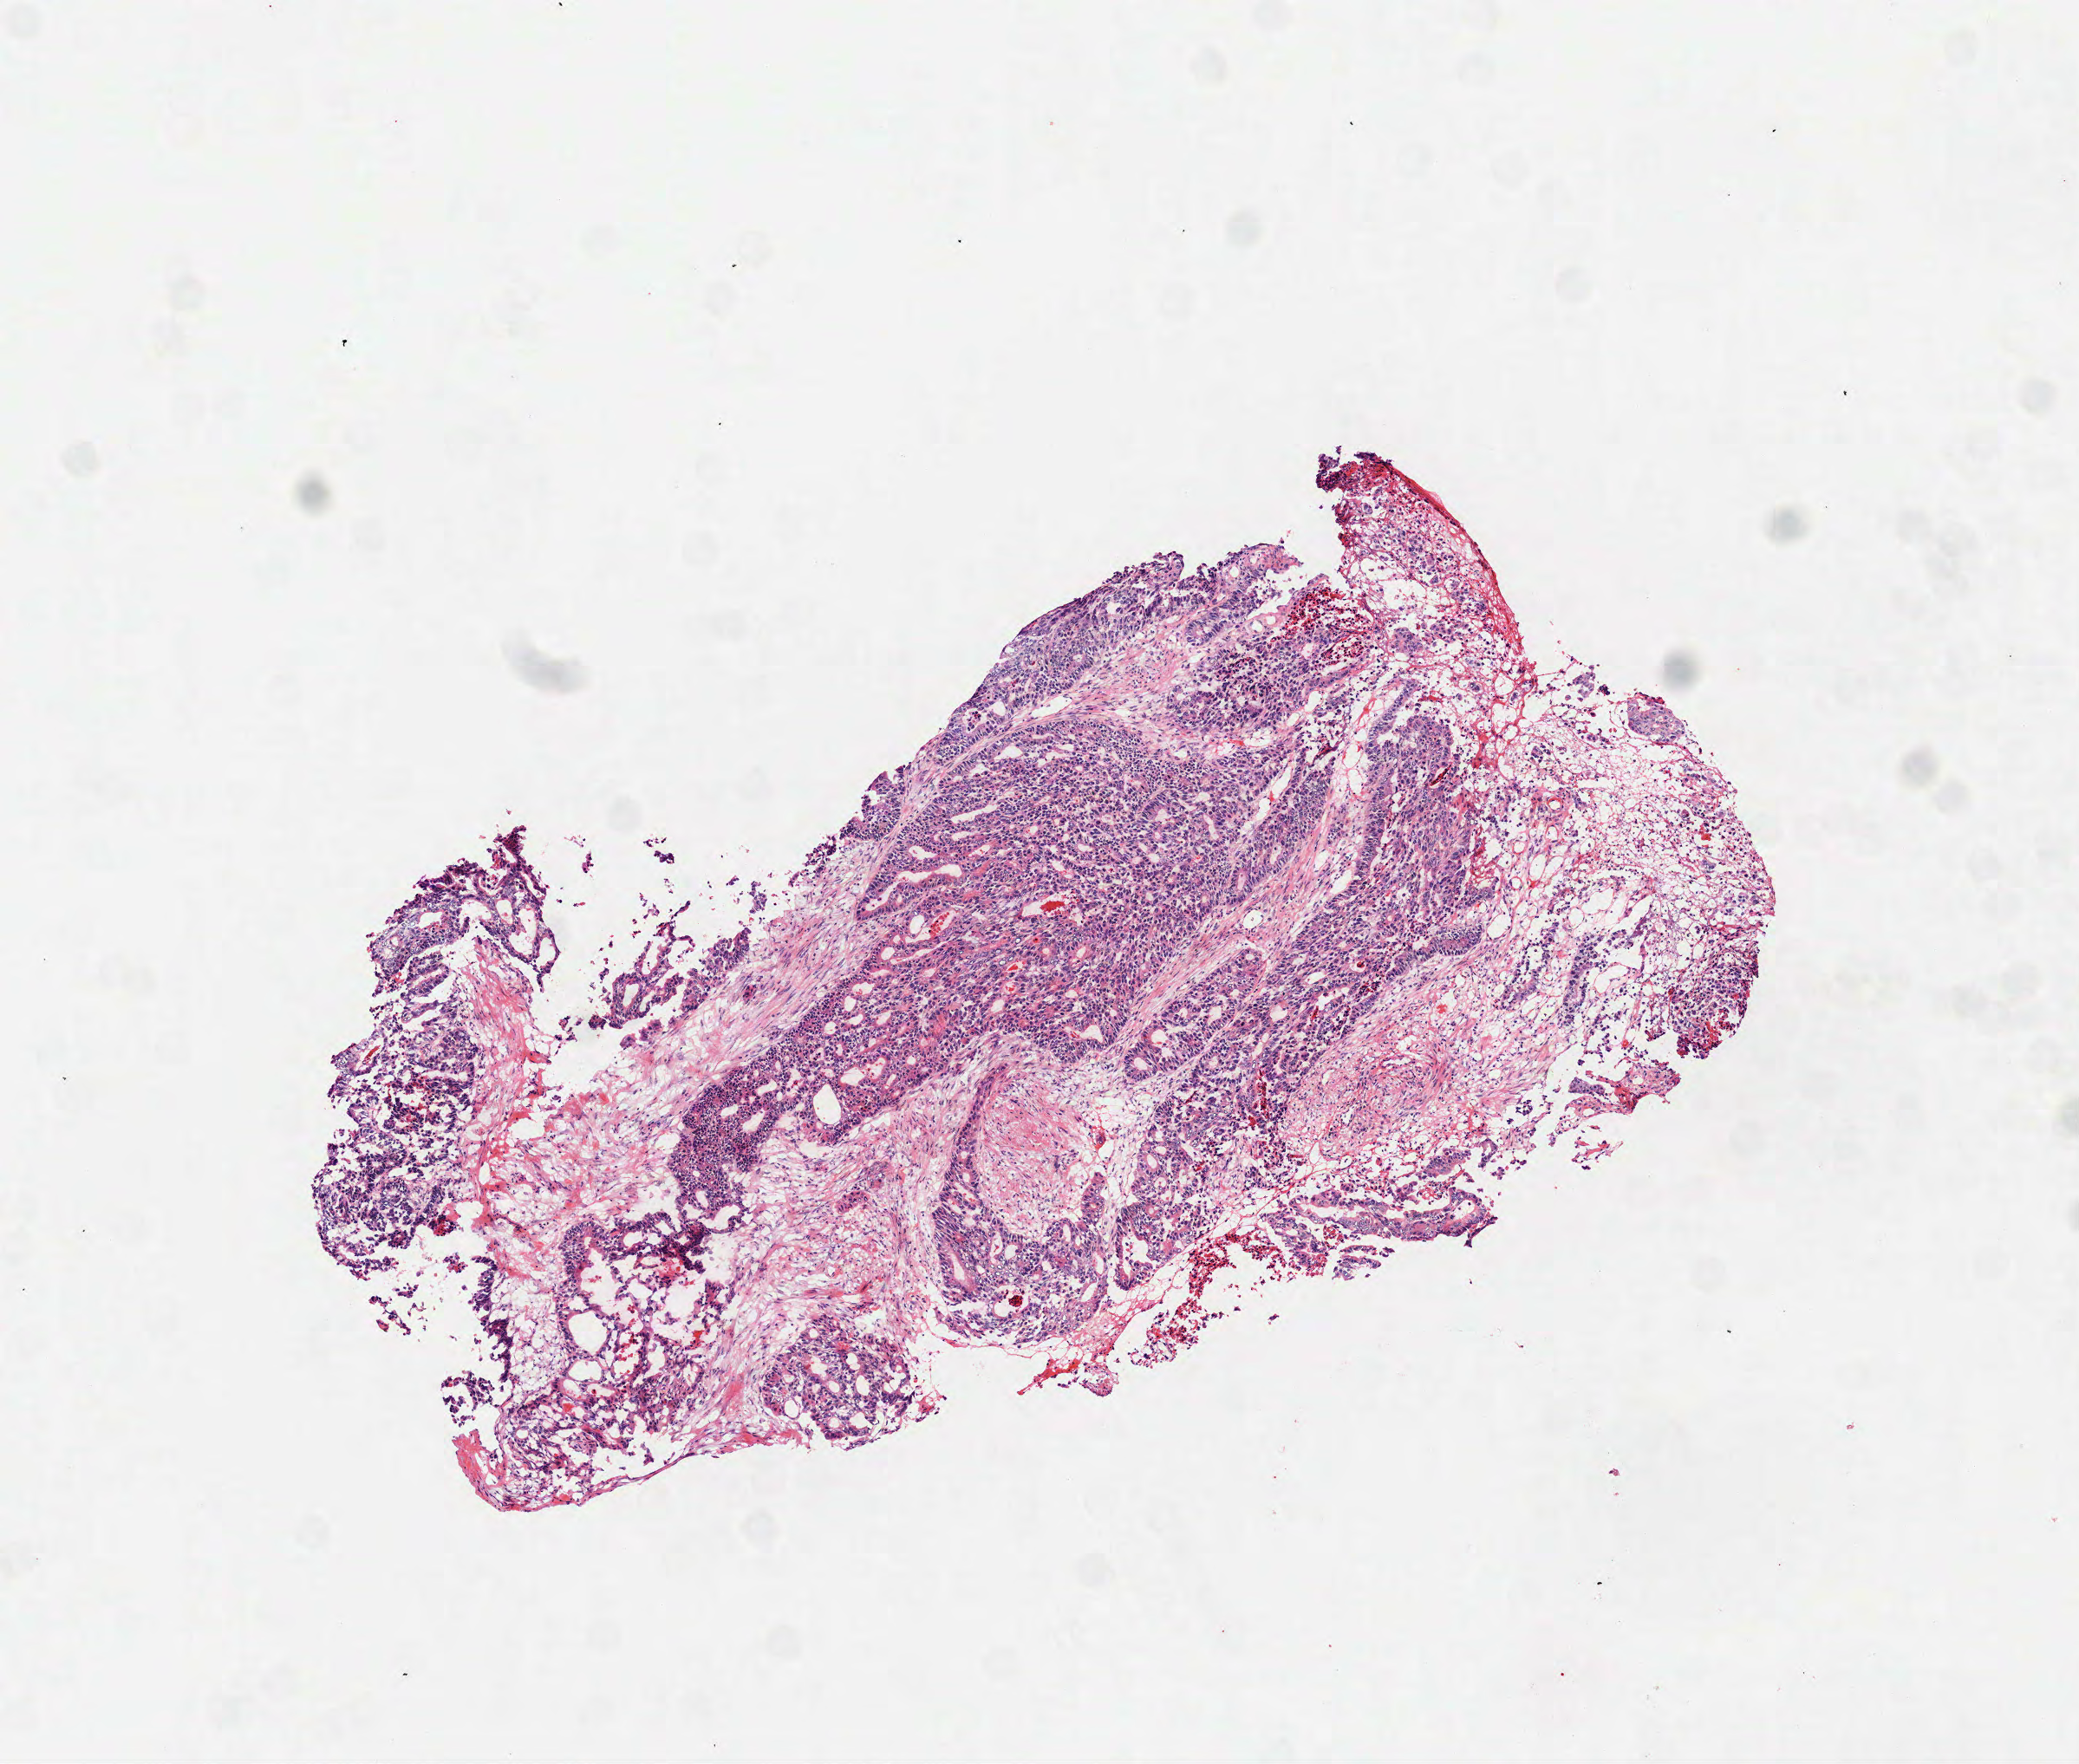
Whole-slide histology image, H&E — low-resolution overview of the scanned area, about 4.8 x 4.1 mm, frozen section from the top of the tissue portion, rectum, primary tumour sample. Female patient; age at initial diagnosis 71 years. Composition of this section per pathologist review: tumour cells 79%, tumour nuclei 80%, normal cells 0%, stromal cells 20%, necrosis 1%.
* AJCC pathologic stage: IIIC
* TNM: T3 N2 MX
* pathologic diagnosis: Adenocarcinoma, NOS (rectosigmoid junction)